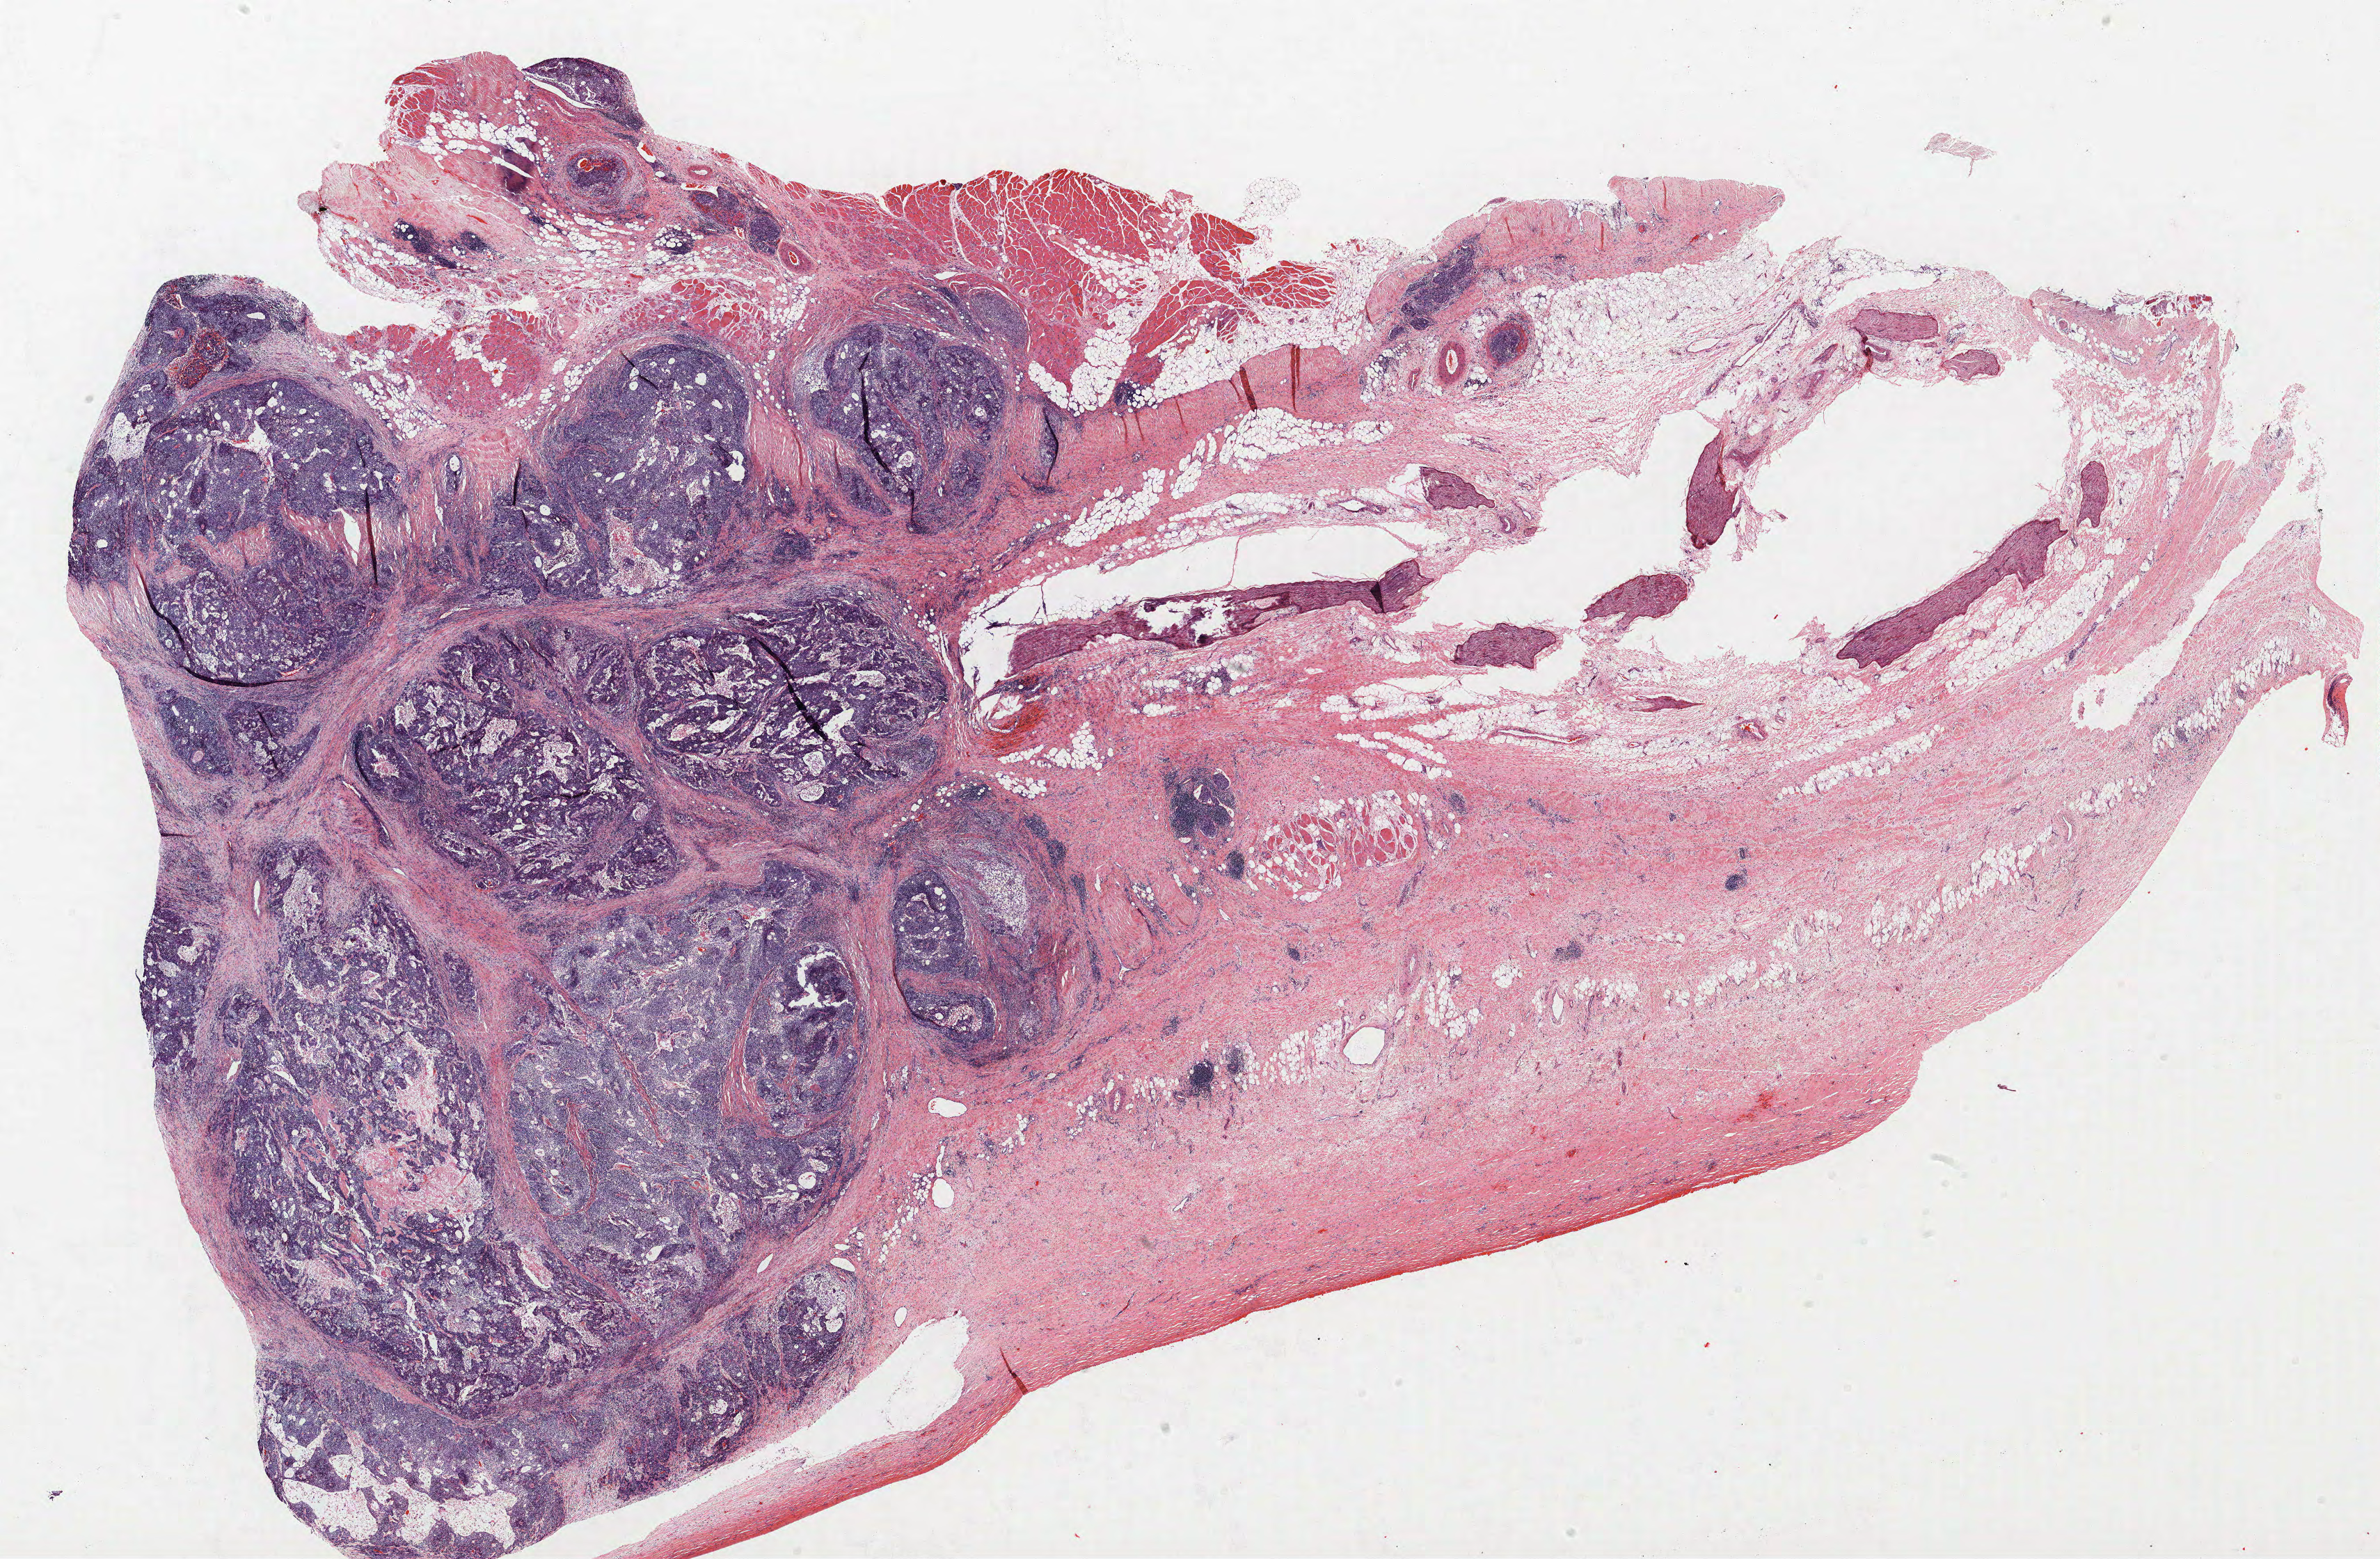
Whole-slide histology image, H&E — a low-resolution overview of the entire scanned area, about 27.4 x 17.9 mm (from a 40x scan), formalin-fixed paraffin-embedded (FFPE) section, lung. Male, age 65 at enrolment. Current smoker at enrolment. Grade: poorly differentiated (G3).
• participant's lung-cancer diagnosis: Non-small cell carcinoma (ICD-O-3 8046/3)
• stage (AJCC 6th edition): IIIB